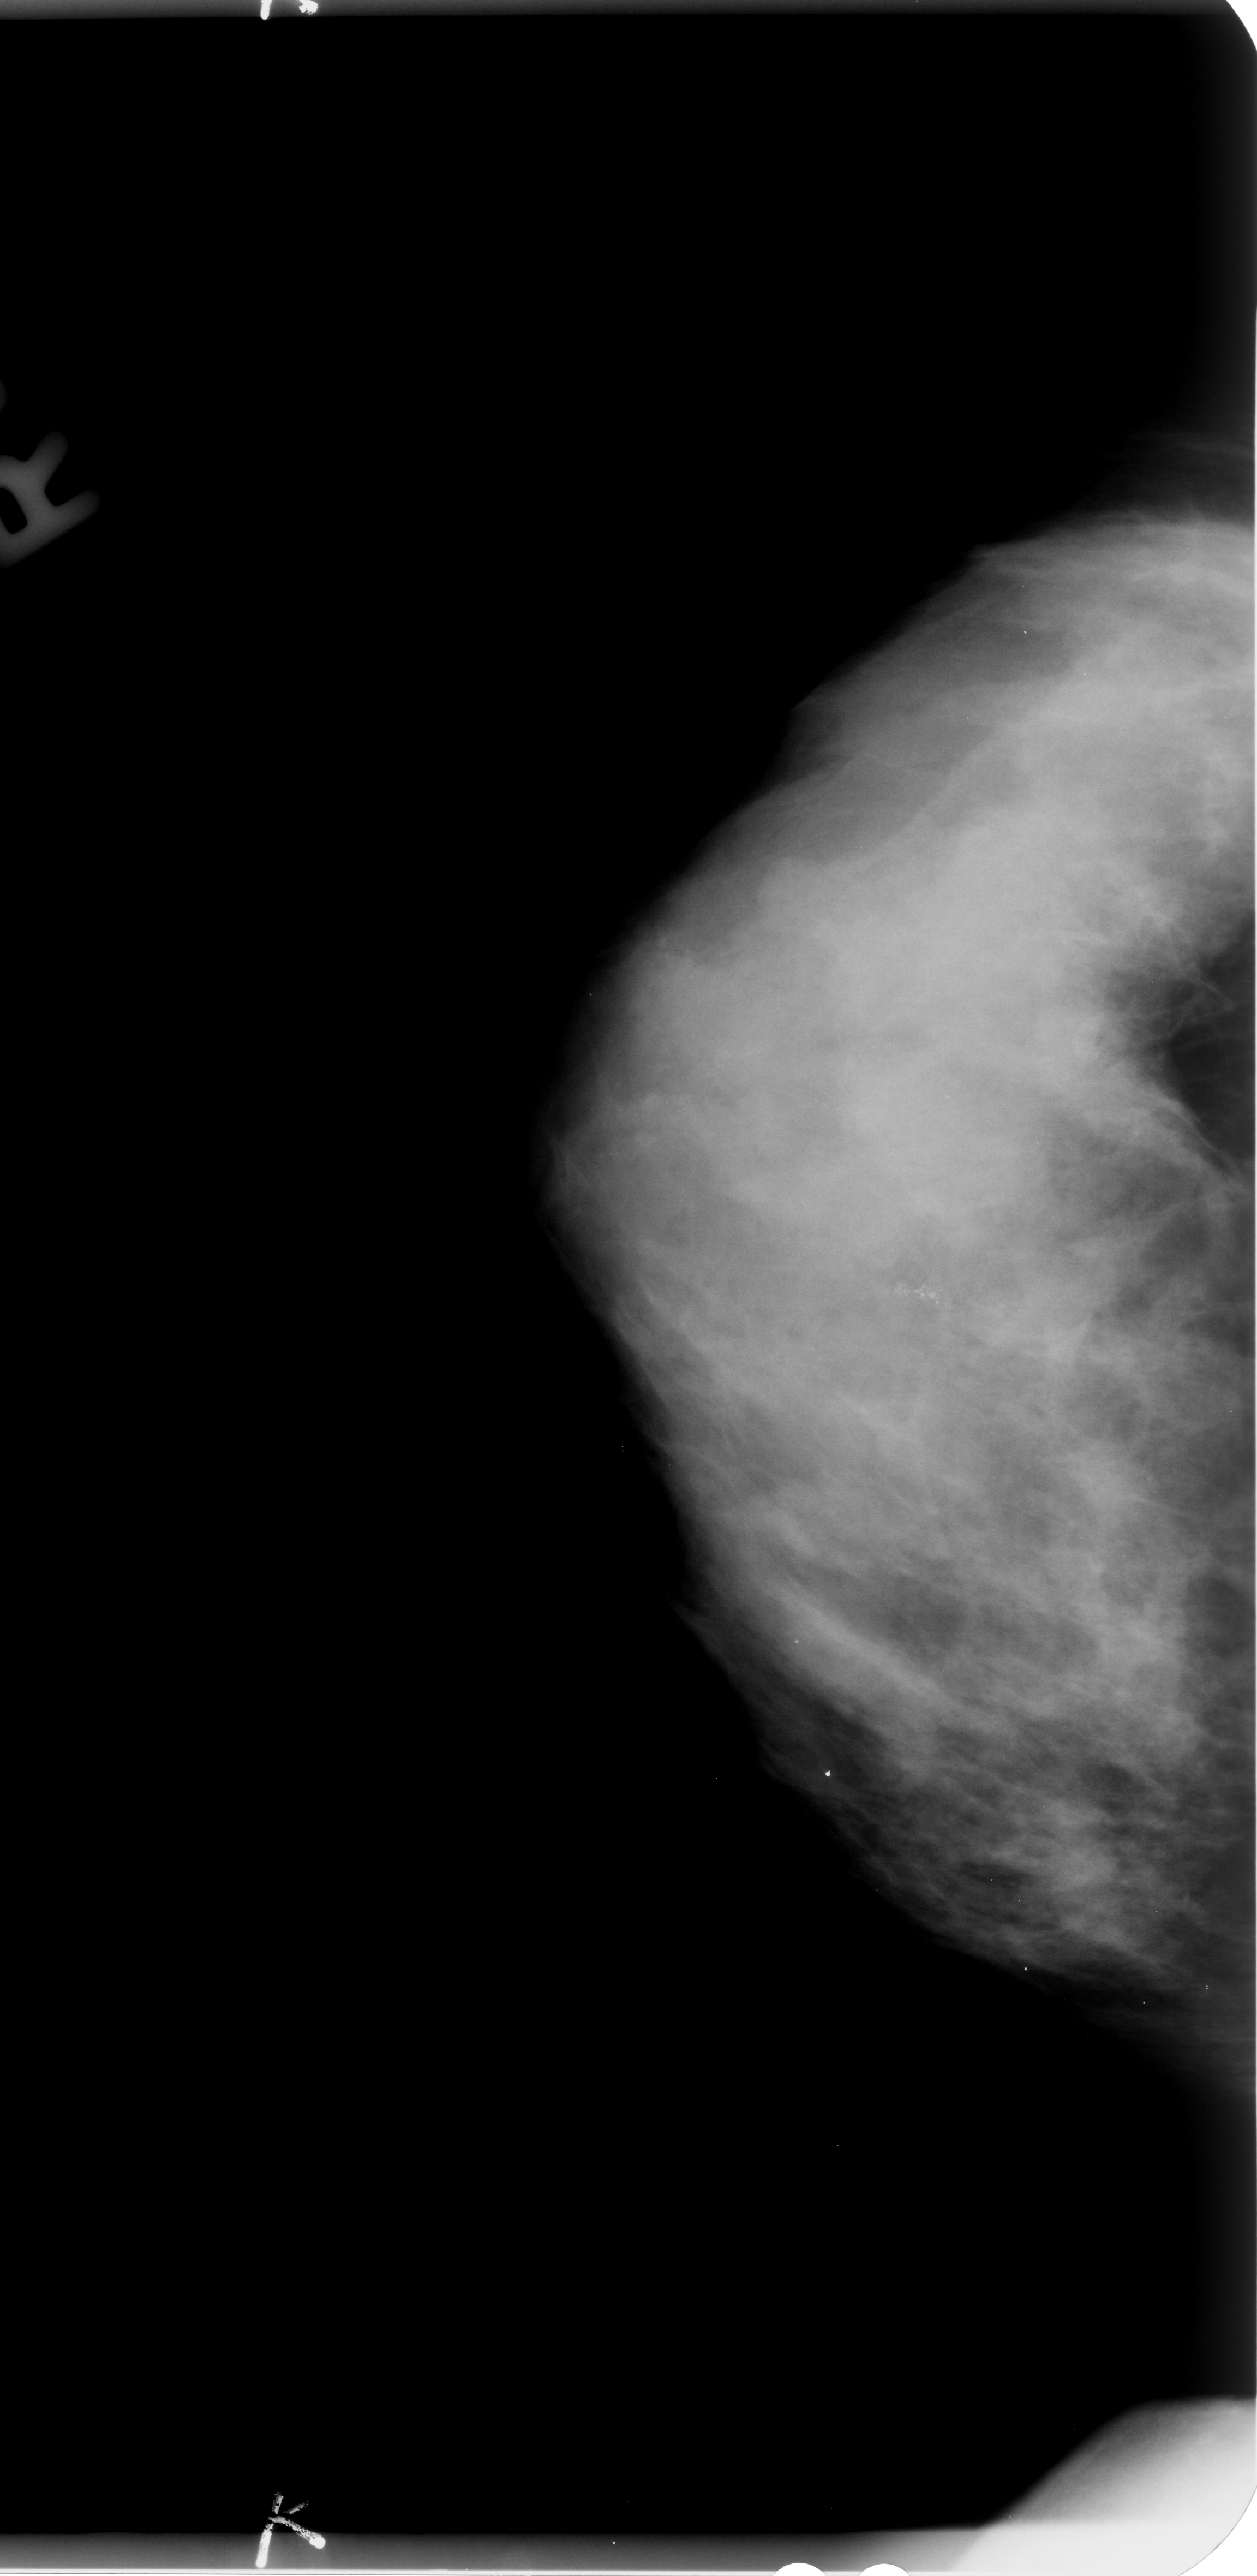
Mammogram (digitized film). Right breast. Craniocaudal (CC) view. BI-RADS breast density category 4 (scale 1–4). 1257 × 2576 image matrix.
Expert-marked regions of interest on this film, with their recorded descriptors:
- calcifications, morphology pleomorphic, distribution clustered; BI-RADS assessment category 4; pathology (as recorded): benign: bounding box [x1, y1, x2, y2] px = [868, 1244, 966, 1346]